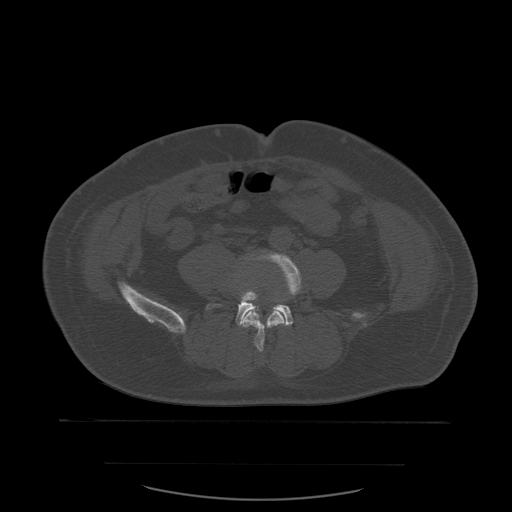
CT including the spine, one axial slice. Slice 152 of 590 in the series (ordered by position). Bone window (W 1800 / L 400 HU). 512 × 512 image matrix. Patient age 71 years. Case-level facts recorded for this patient, not image findings: primary cancer: lung; vertebrae with lytic lesions (as recorded): T1, T2, L5, S1.
Outlined on this slice (semi-automatic segmentation, software-assisted and operator-edited):
- L4 vertebra: bounding box (x1, y1, x2, y2) in pixels: (243, 251, 302, 352)
- L5 vertebra: (207, 287, 294, 327)